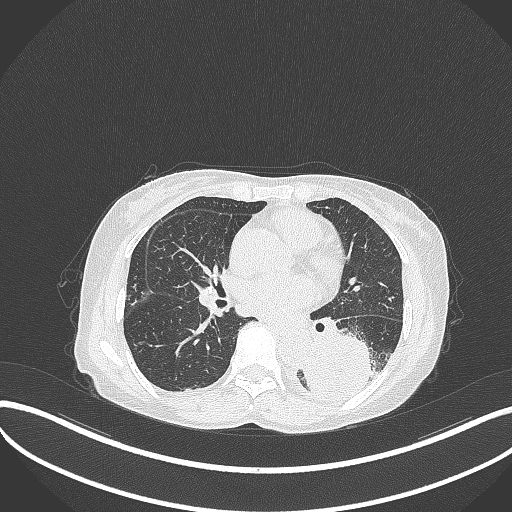
Chest CT, one axial slice. Position 151 of 370 along the scan axis. 120 kVp. Lung window (W 1500 / L -600 HU). 1 mm slice thickness. 512 × 512 image matrix. Patient: female, 78 years. From the clinical record (not read from this slice): clinical TNM (as recorded): T3 N0 M1.
Annotated regions visible in this slice (rectangle marked by the reading radiologist):
- lung tumour (recorded histology: squamous cell carcinoma): bounding box [x1, y1, x2, y2] px = [302, 331, 390, 400]